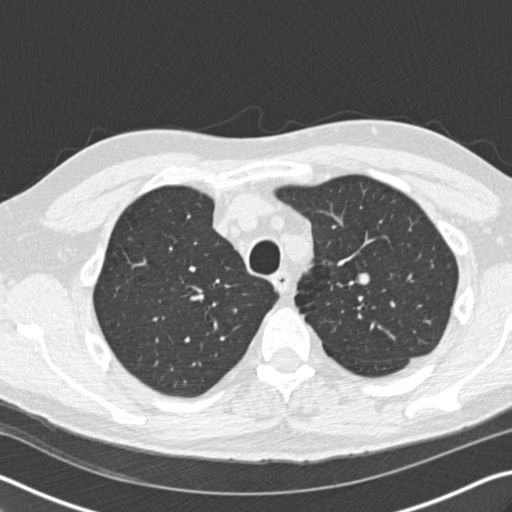
Low-dose screening chest CT, axial slice; baseline annual screen; lung window (W 1500 / L -600 HU). Male, age 56 years at enrolment. Current smoker at enrolment.
Expert-annotated lung lesion, box from (x=329, y=260) to (x=392, y=308) px. Reader record for this screening exam (exam-level; its link to the box is not recorded): non-calcified nodule or mass ≥4 mm, left upper lobe, 12 × 10 mm, smooth margins, soft tissue attenuation. Participant outcome: lung cancer diagnosed 814 days after this screen (after the third annual screen) — neuroendocrine carcinoma, NOS, left upper lobe, well differentiated (G1), stage IA (AJCC 6th edition), 20 mm at pathology.